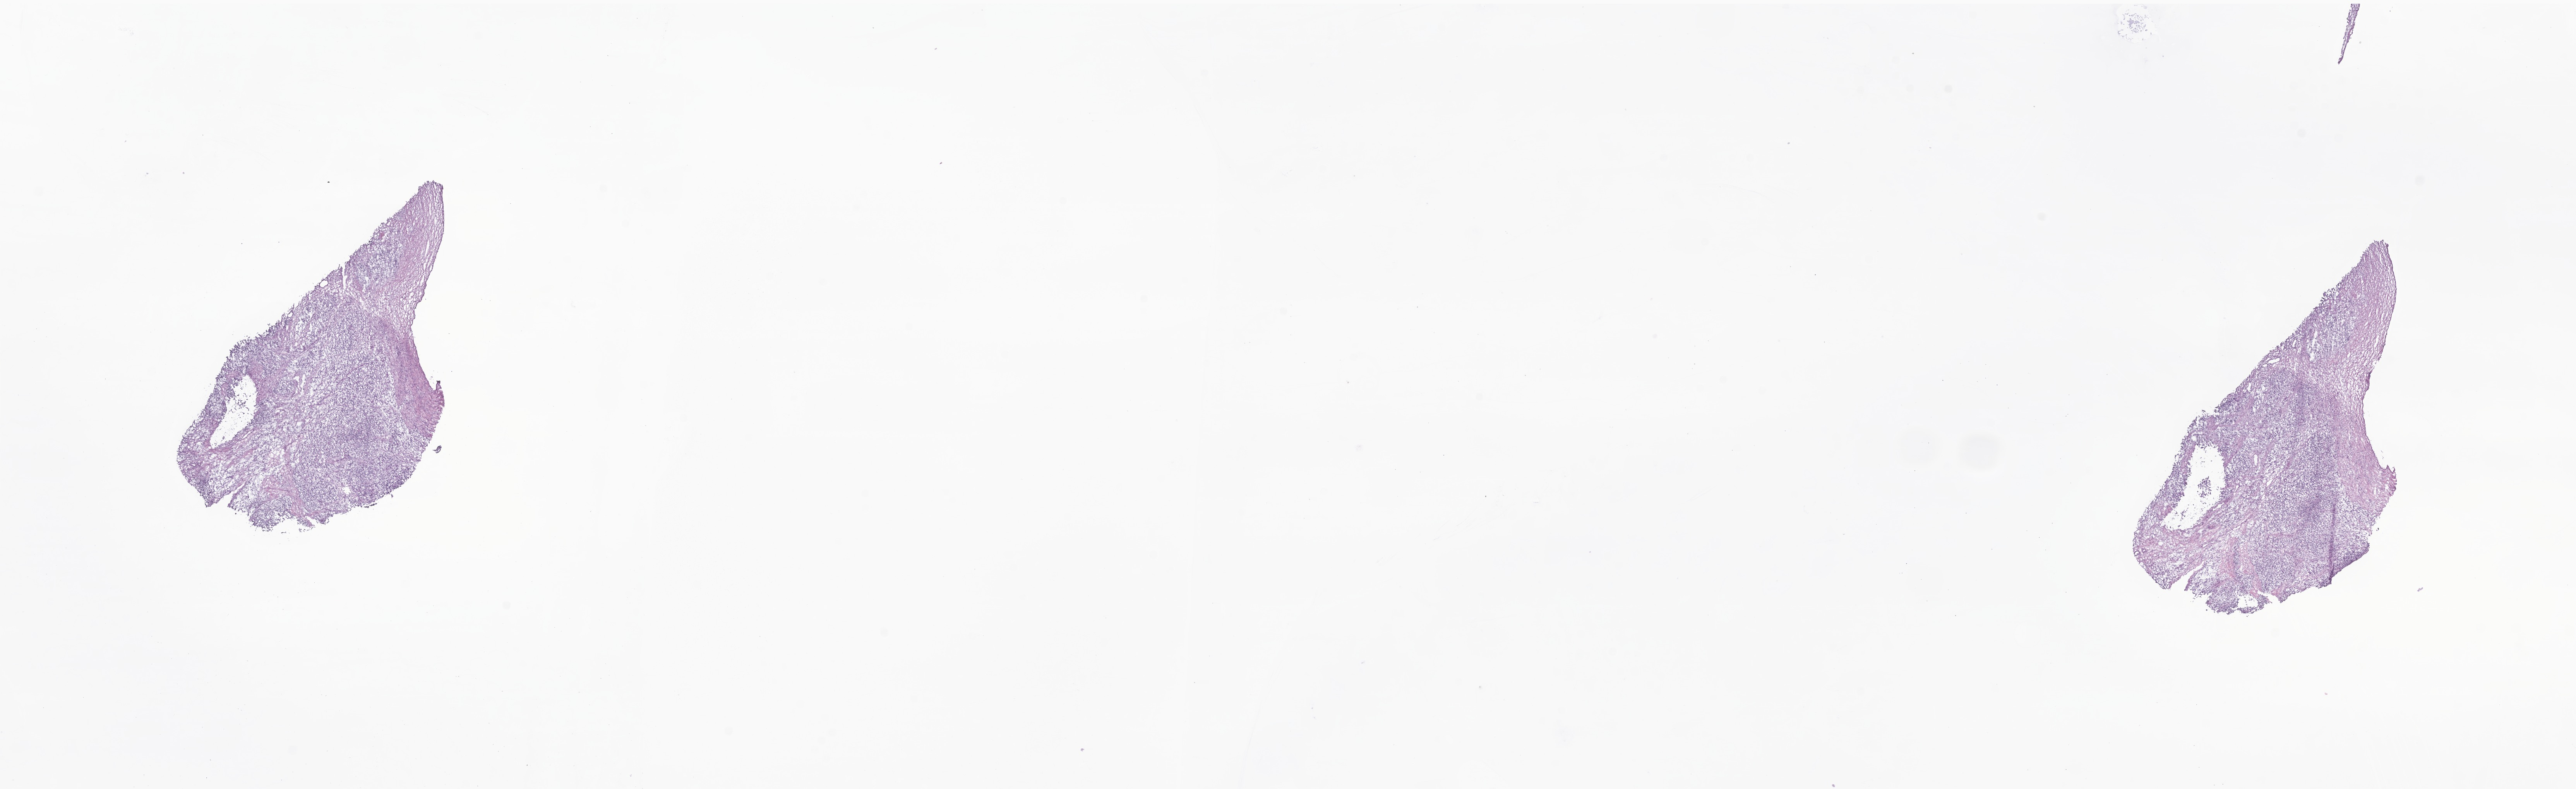
Haematoxylin and eosin whole-slide image of tumor tissue from the testis — whole scanned area (about 28.1 x 8.6 mm) shown as a low-resolution overview; cryosection (OCT / tissue freezing medium). Patient: male, age 187 months.
Recorded diagnosis: Embryonal rhabdomyosarcoma, NOS.